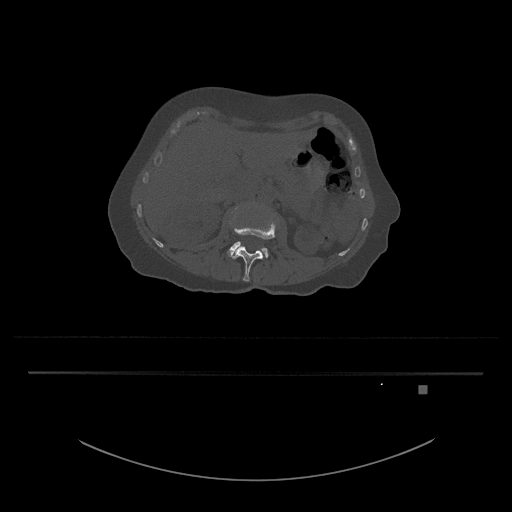
CT including the spine, one axial slice. Position 473 of 797 along the scan axis. 120 kVp. Bone window (W 1800 / L 400 HU). 0.5 mm slice thickness. 512 × 512 image matrix, field of view 500 × 500 mm. Female patient, age 57 years. From the clinical record (not read from this slice): primary cancer: cervical.
Outlined on this slice (semi-automatic segmentation, software-assisted and operator-edited):
- L3 vertebra: box from (x=227, y=206) to (x=269, y=259) px